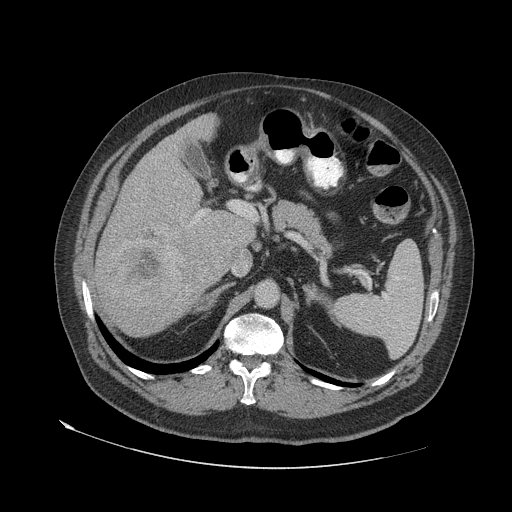
Contrast-enhanced abdominal CT (liver protocol), one axial slice; position 35 of 79 along the scan axis; reconstruction kernel STANDARD; 140 kVp; soft-tissue window (W 400 / L 40 HU); 2.5 mm slice thickness; 512 × 512 image matrix, field of view 480 × 480 mm. From the clinical record (not read from this slice): diagnosis: hepatocellular carcinoma (patient treated with transarterial chemoembolisation; whether this scan precedes or follows treatment is not stated here); TNM stage (as recorded): Stage-IVA; Child-Pugh class: A.
Annotated regions visible in this slice (semi-automatically segmented with operator editing):
- liver parenchyma outside the tumour (the mass and vessels are separate outlines, so this box may not span the whole liver): bounding box [x1, y1, x2, y2] px = [92, 114, 258, 336]
- mass: [101, 229, 188, 308]
- liver vessels: [196, 209, 256, 271]